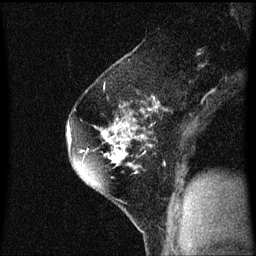
Breast MRI (dynamic contrast-enhanced), one sagittal slice; position 41 of 60 along the scan axis; dynamic contrast-enhanced series, image 2 of 3 at this slice position (ordered by acquisition); 1.5 T; TE 4.2 ms, TR 8.4 ms; 256 × 256 image matrix, field of view 200 × 200 mm. Patient: female, 60 years.
Annotated regions visible in this slice (semi-automatically segmented with operator editing):
- analysis volume of interest (the breast-tissue region the enhancement analysis was run in; not a lesion): bounding box [x1, y1, x2, y2] px = [66, 70, 145, 193]
- tumour enhancement mask (voxels above the 70 % enhancement threshold inside the analysis volume of interest): [68, 110, 143, 185]